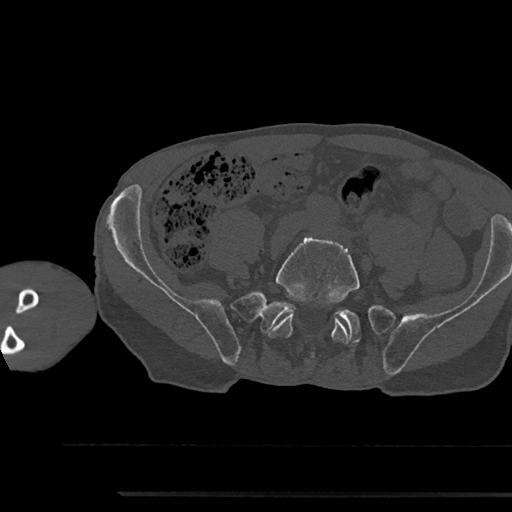
CT including the spine, one axial slice; position 329 of 797 along the scan axis; bone window (W 1800 / L 400 HU); 512 × 512 image matrix. Male patient, age 79 years. Case-level facts recorded for this patient, not image findings: primary cancer: prostate.
Structures marked on this image (semi-automatically segmented with operator editing):
- L5 vertebra: bounding box <267,237,360,362> (left, top, right, bottom; pixels)